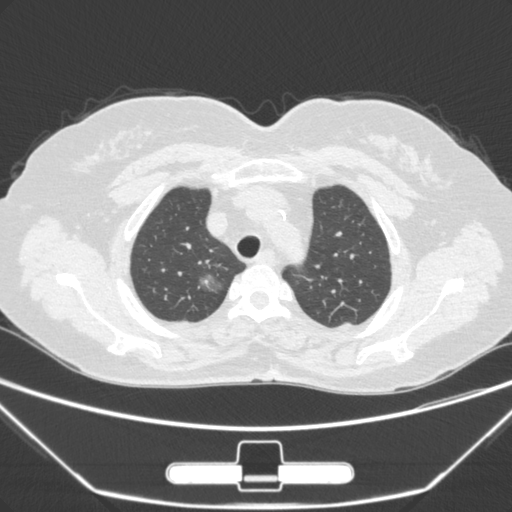
Chest CT, one axial slice; position 228 of 275 along the scan axis; 120 kVp; lung window (W 1500 / L -600 HU); 1 mm slice thickness; 512 × 512 image matrix. Female patient, age 63 years. From the clinical record (not read from this slice): clinical TNM (as recorded): T1a N0 M0; histopathological grade: G1.
Outlined on this slice (bounding box drawn by a radiologist):
- lung tumour (recorded histology: adenocarcinoma): box from (x=195, y=272) to (x=230, y=304) px